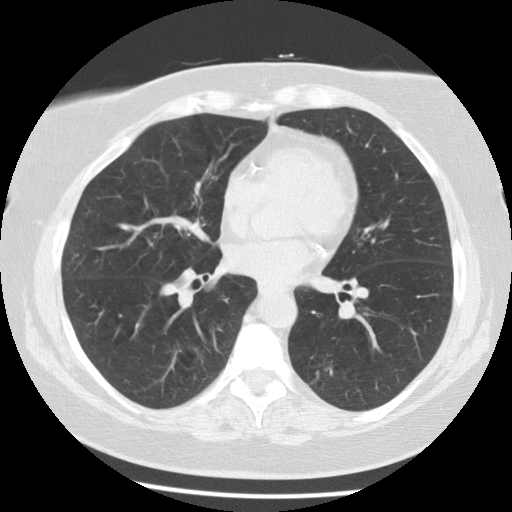
Low-dose screening chest CT, axial slice. Third annual screen. Lung window (W 1500 / L -600 HU). 2.5 mm slice thickness. Standard (soft-tissue) reconstruction kernel (STANDARD). 120 kVp. Slice 63 of 116 in the series. 512 × 512 image matrix, field of view 341 × 341 mm. Female participant, aged 59 years at enrolment. Current smoker at enrolment.
• Expert reader's lesion annotation, box from (x=284, y=346) to (x=356, y=406) px.
• The screening reader recorded 6 non-calcified nodules or masses ≥4 mm on this exam; which of them this box marks is not recorded.
• Lung cancer was diagnosed 56 days after this screen: adenocarcinoma, NOS, left lower lobe, poorly differentiated (G3), stage IA (AJCC 6th edition), 15 mm at pathology.